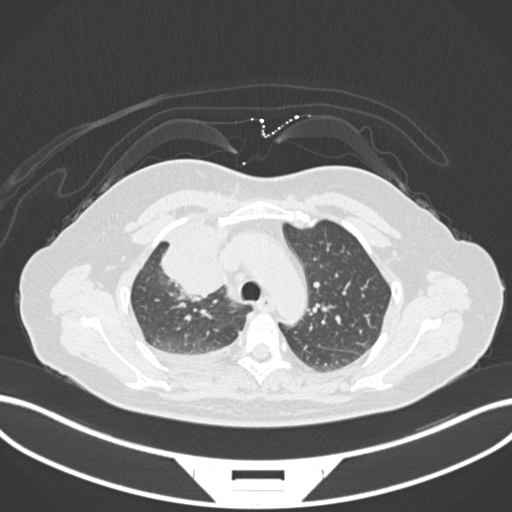
Chest CT, one axial slice. Slice 117 of 172 in the series (ordered by position). Lung window (W 1500 / L -600 HU). 1 mm slice thickness. 512 × 512 image matrix. Female patient, age 52 years. Case-level facts recorded for this patient, not image findings: clinical TNM (as recorded): T3 N1 M1.
Annotated regions visible in this slice (rectangle marked by the reading radiologist):
- lung tumour (recorded histology: adenocarcinoma): box from (x=158, y=218) to (x=225, y=299) px